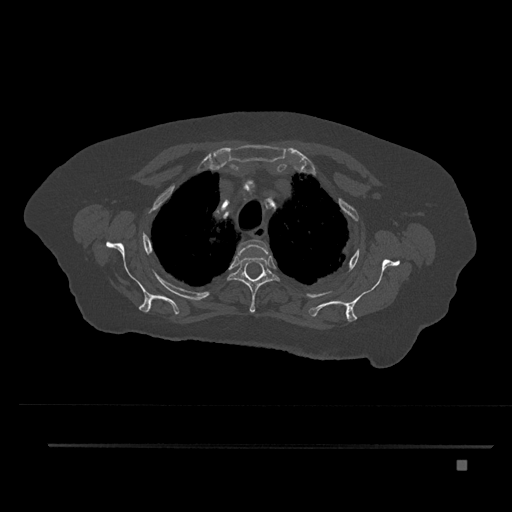
CT including the spine, one axial slice. Position 641 of 797 along the scan axis. 120 kVp. Bone window (W 1800 / L 400 HU). 512 × 512 image matrix, field of view 437 × 437 mm. Female patient, age 76 years. From the clinical record (not read from this slice): primary cancer: lung.
Outlined on this slice (semi-automatically segmented with operator editing):
- T2 vertebra: bounding box (x1, y1, x2, y2) in pixels: (236, 239, 270, 257)
- T3 vertebra: (227, 256, 280, 313)